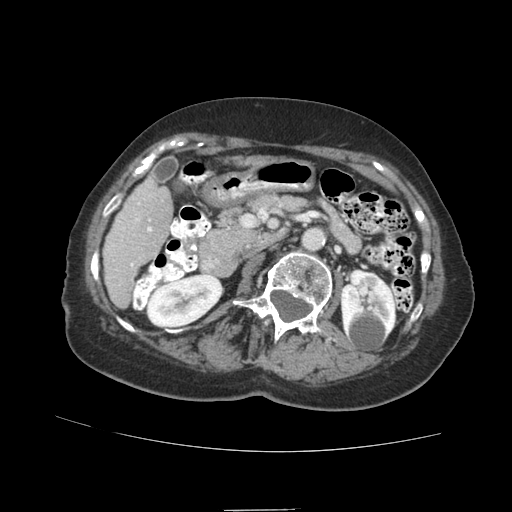
Contrast-enhanced abdominal CT (liver protocol), one axial slice. Position 29 of 89 along the scan axis. Soft-tissue window (W 400 / L 40 HU). 2.5 mm slice thickness. 512 × 512 image matrix, field of view 360 × 360 mm. From the clinical record (not read from this slice): diagnosis: hepatocellular carcinoma (patient treated with transarterial chemoembolisation; whether this scan precedes or follows treatment is not stated here); TNM stage (as recorded): Stage-II; Child-Pugh class: A.
Structures marked on this image (semi-automatically segmented with operator editing):
- liver parenchyma outside the tumour (the mass and vessels are separate outlines, so this box may not span the whole liver): bounding box [x1, y1, x2, y2] px = [102, 176, 172, 308]
- liver vessels: [118, 203, 152, 266]